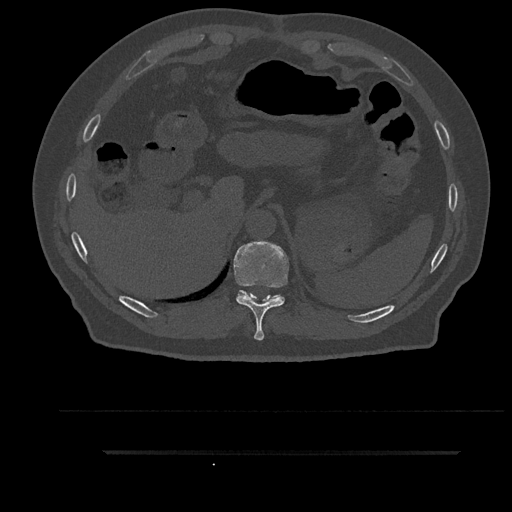
CT including the spine, one axial slice. Position 349 of 797 along the scan axis. Reconstruction kernel Br40s/3. Bone window (W 1800 / L 400 HU). 0.5 mm slice thickness. 512 × 512 image matrix. Male patient, age 63 years. From the clinical record (not read from this slice): primary cancer: renal; vertebrae with lytic lesions (as recorded): T8.
Annotated regions visible in this slice (semi-automatically segmented with operator editing):
- T10 vertebra: bounding box <233,241,289,341> (left, top, right, bottom; pixels)
- T11 vertebra: <239,290,280,300>